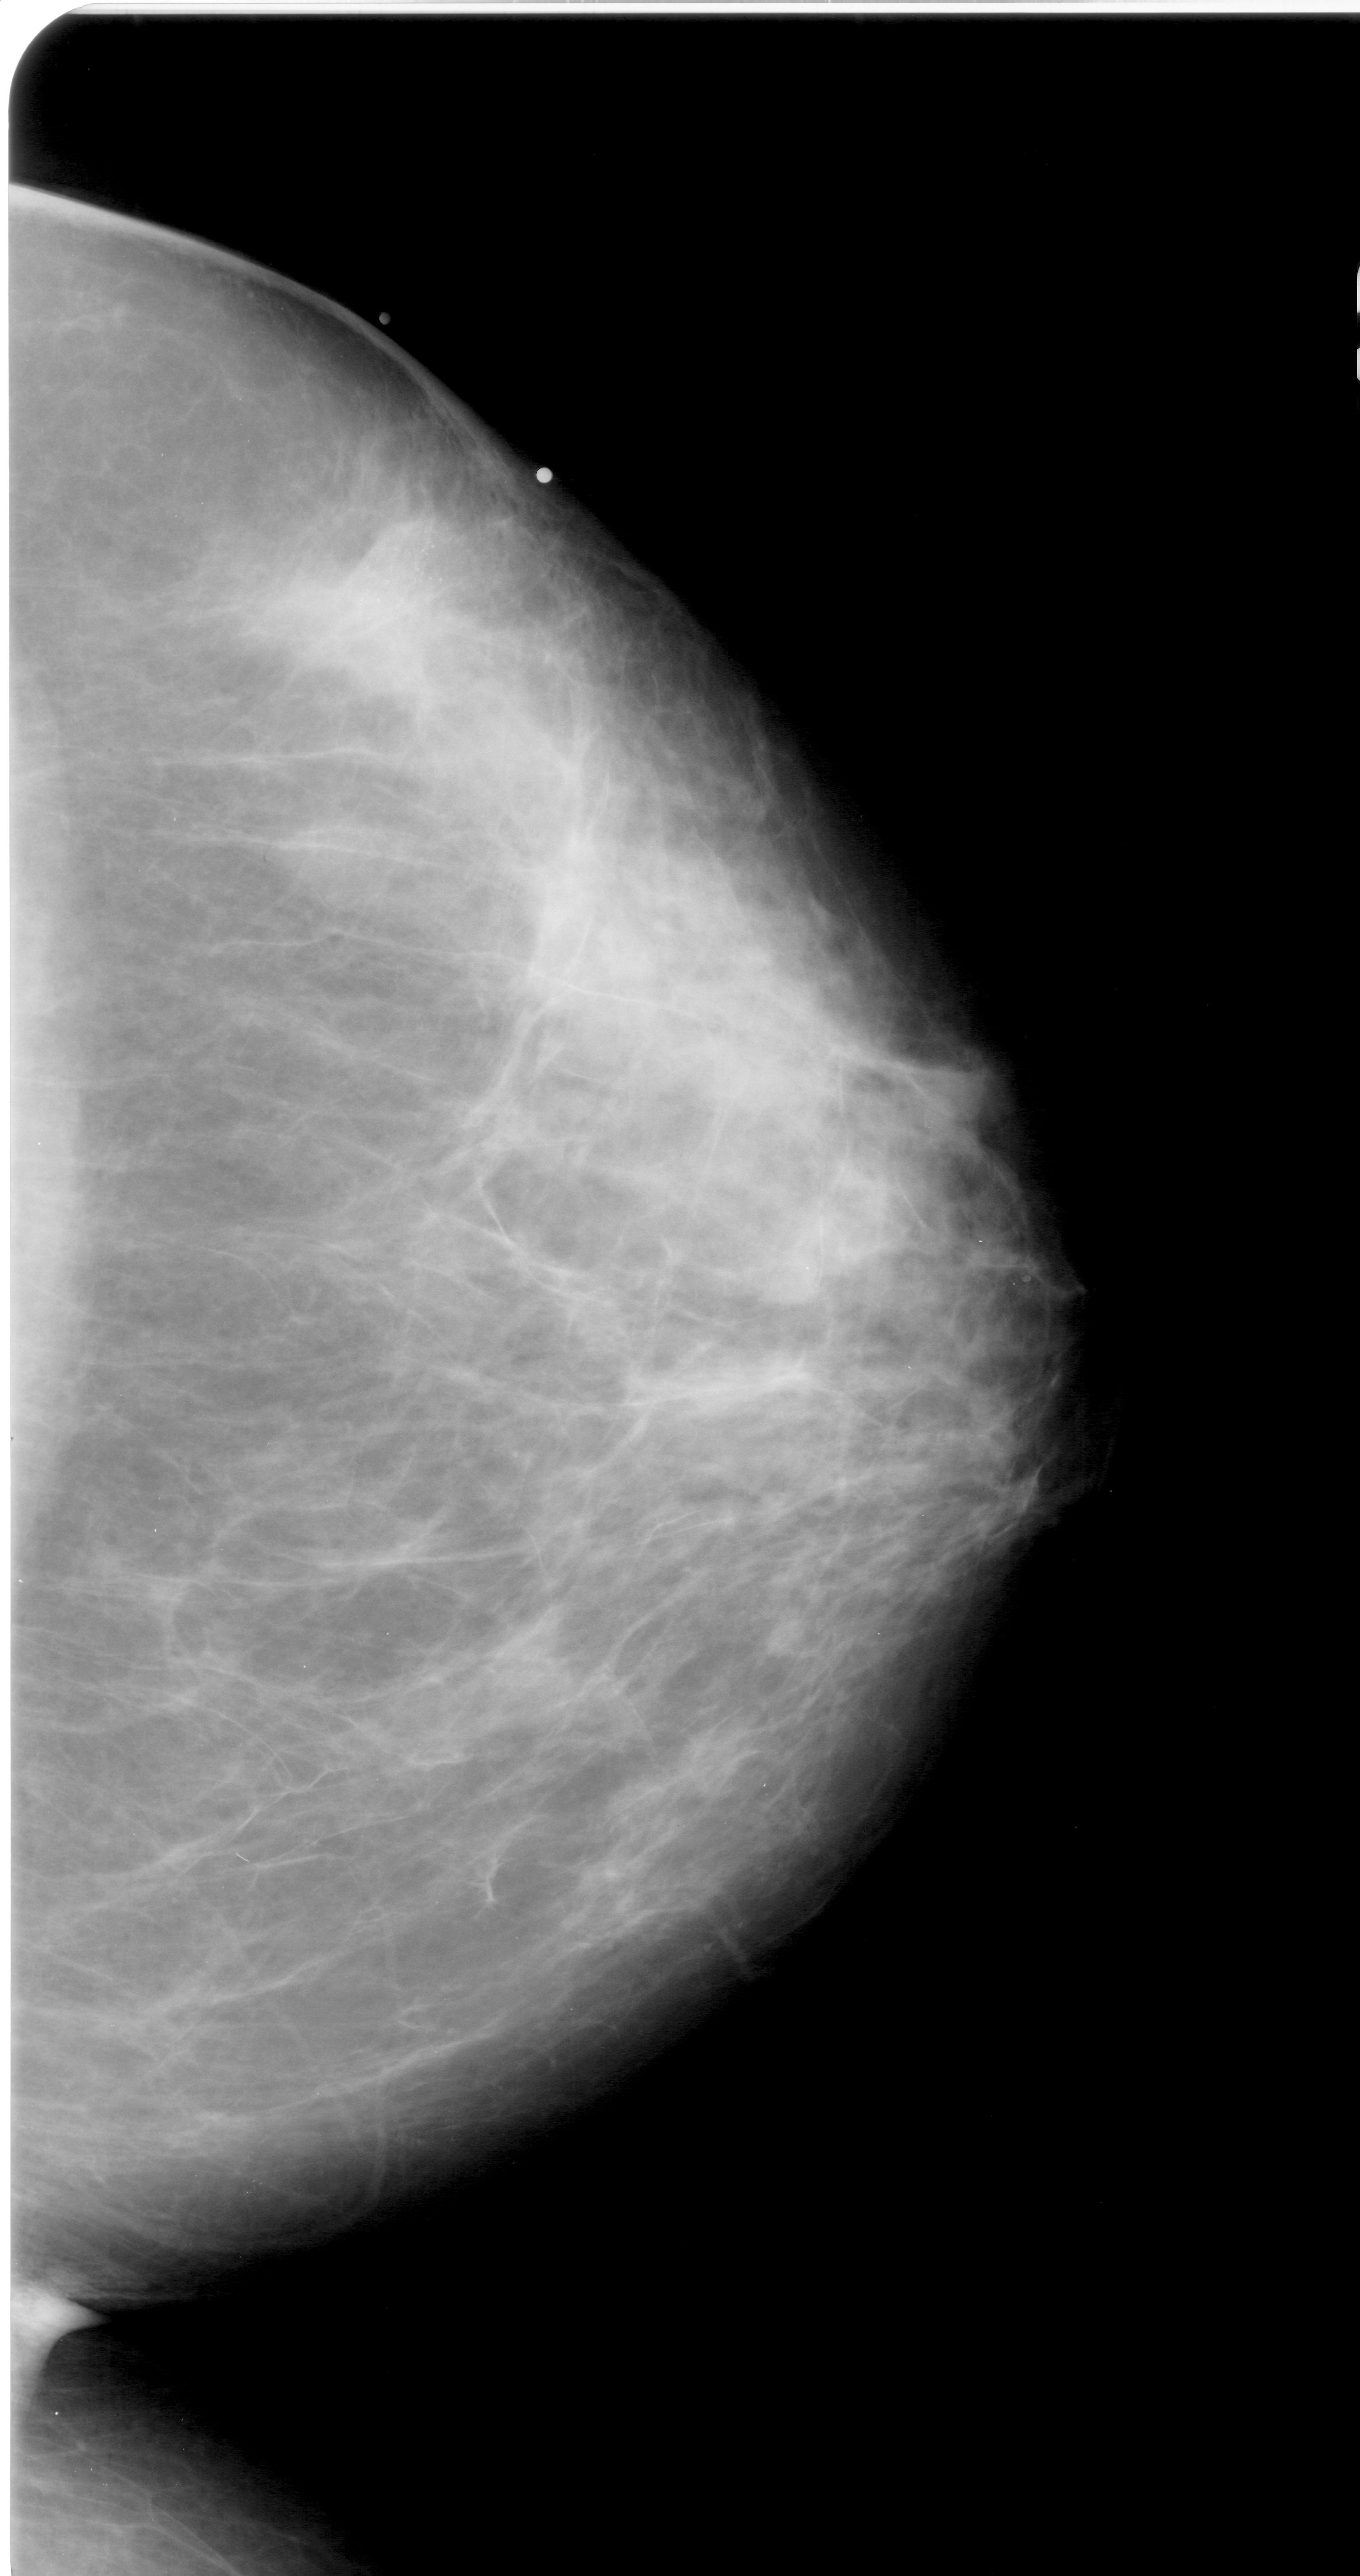
Mammogram (digitized film); right breast; craniocaudal (CC) view; breast composition: heterogeneously dense (BI-RADS density category 3 of 4); 1360 × 2576 image matrix.
Expert-marked regions of interest on this film, with their recorded descriptors:
- mass, shape irregular, margins spiculated; BI-RADS assessment category 5; pathology result (as recorded, not read from the image): malignant: bounding box <317,501,491,660> (left, top, right, bottom; pixels)